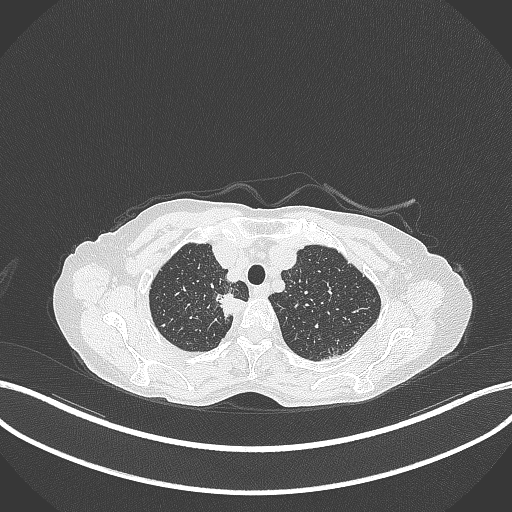
Chest CT, one axial slice. Slice 315 of 403 in the series (ordered by position). Reconstruction kernel B70f. 120 kVp. Lung window (W 1500 / L -600 HU). 1 mm slice thickness. 512 × 512 image matrix, field of view 400 × 400 mm. Patient: female, 75 years. From the clinical record (not read from this slice): clinical TNM (as recorded): T1c N1 M1.
Annotated regions visible in this slice (bounding box drawn by a radiologist):
- lung tumour (recorded histology: adenocarcinoma): bounding box [x1, y1, x2, y2] px = [212, 291, 251, 321]